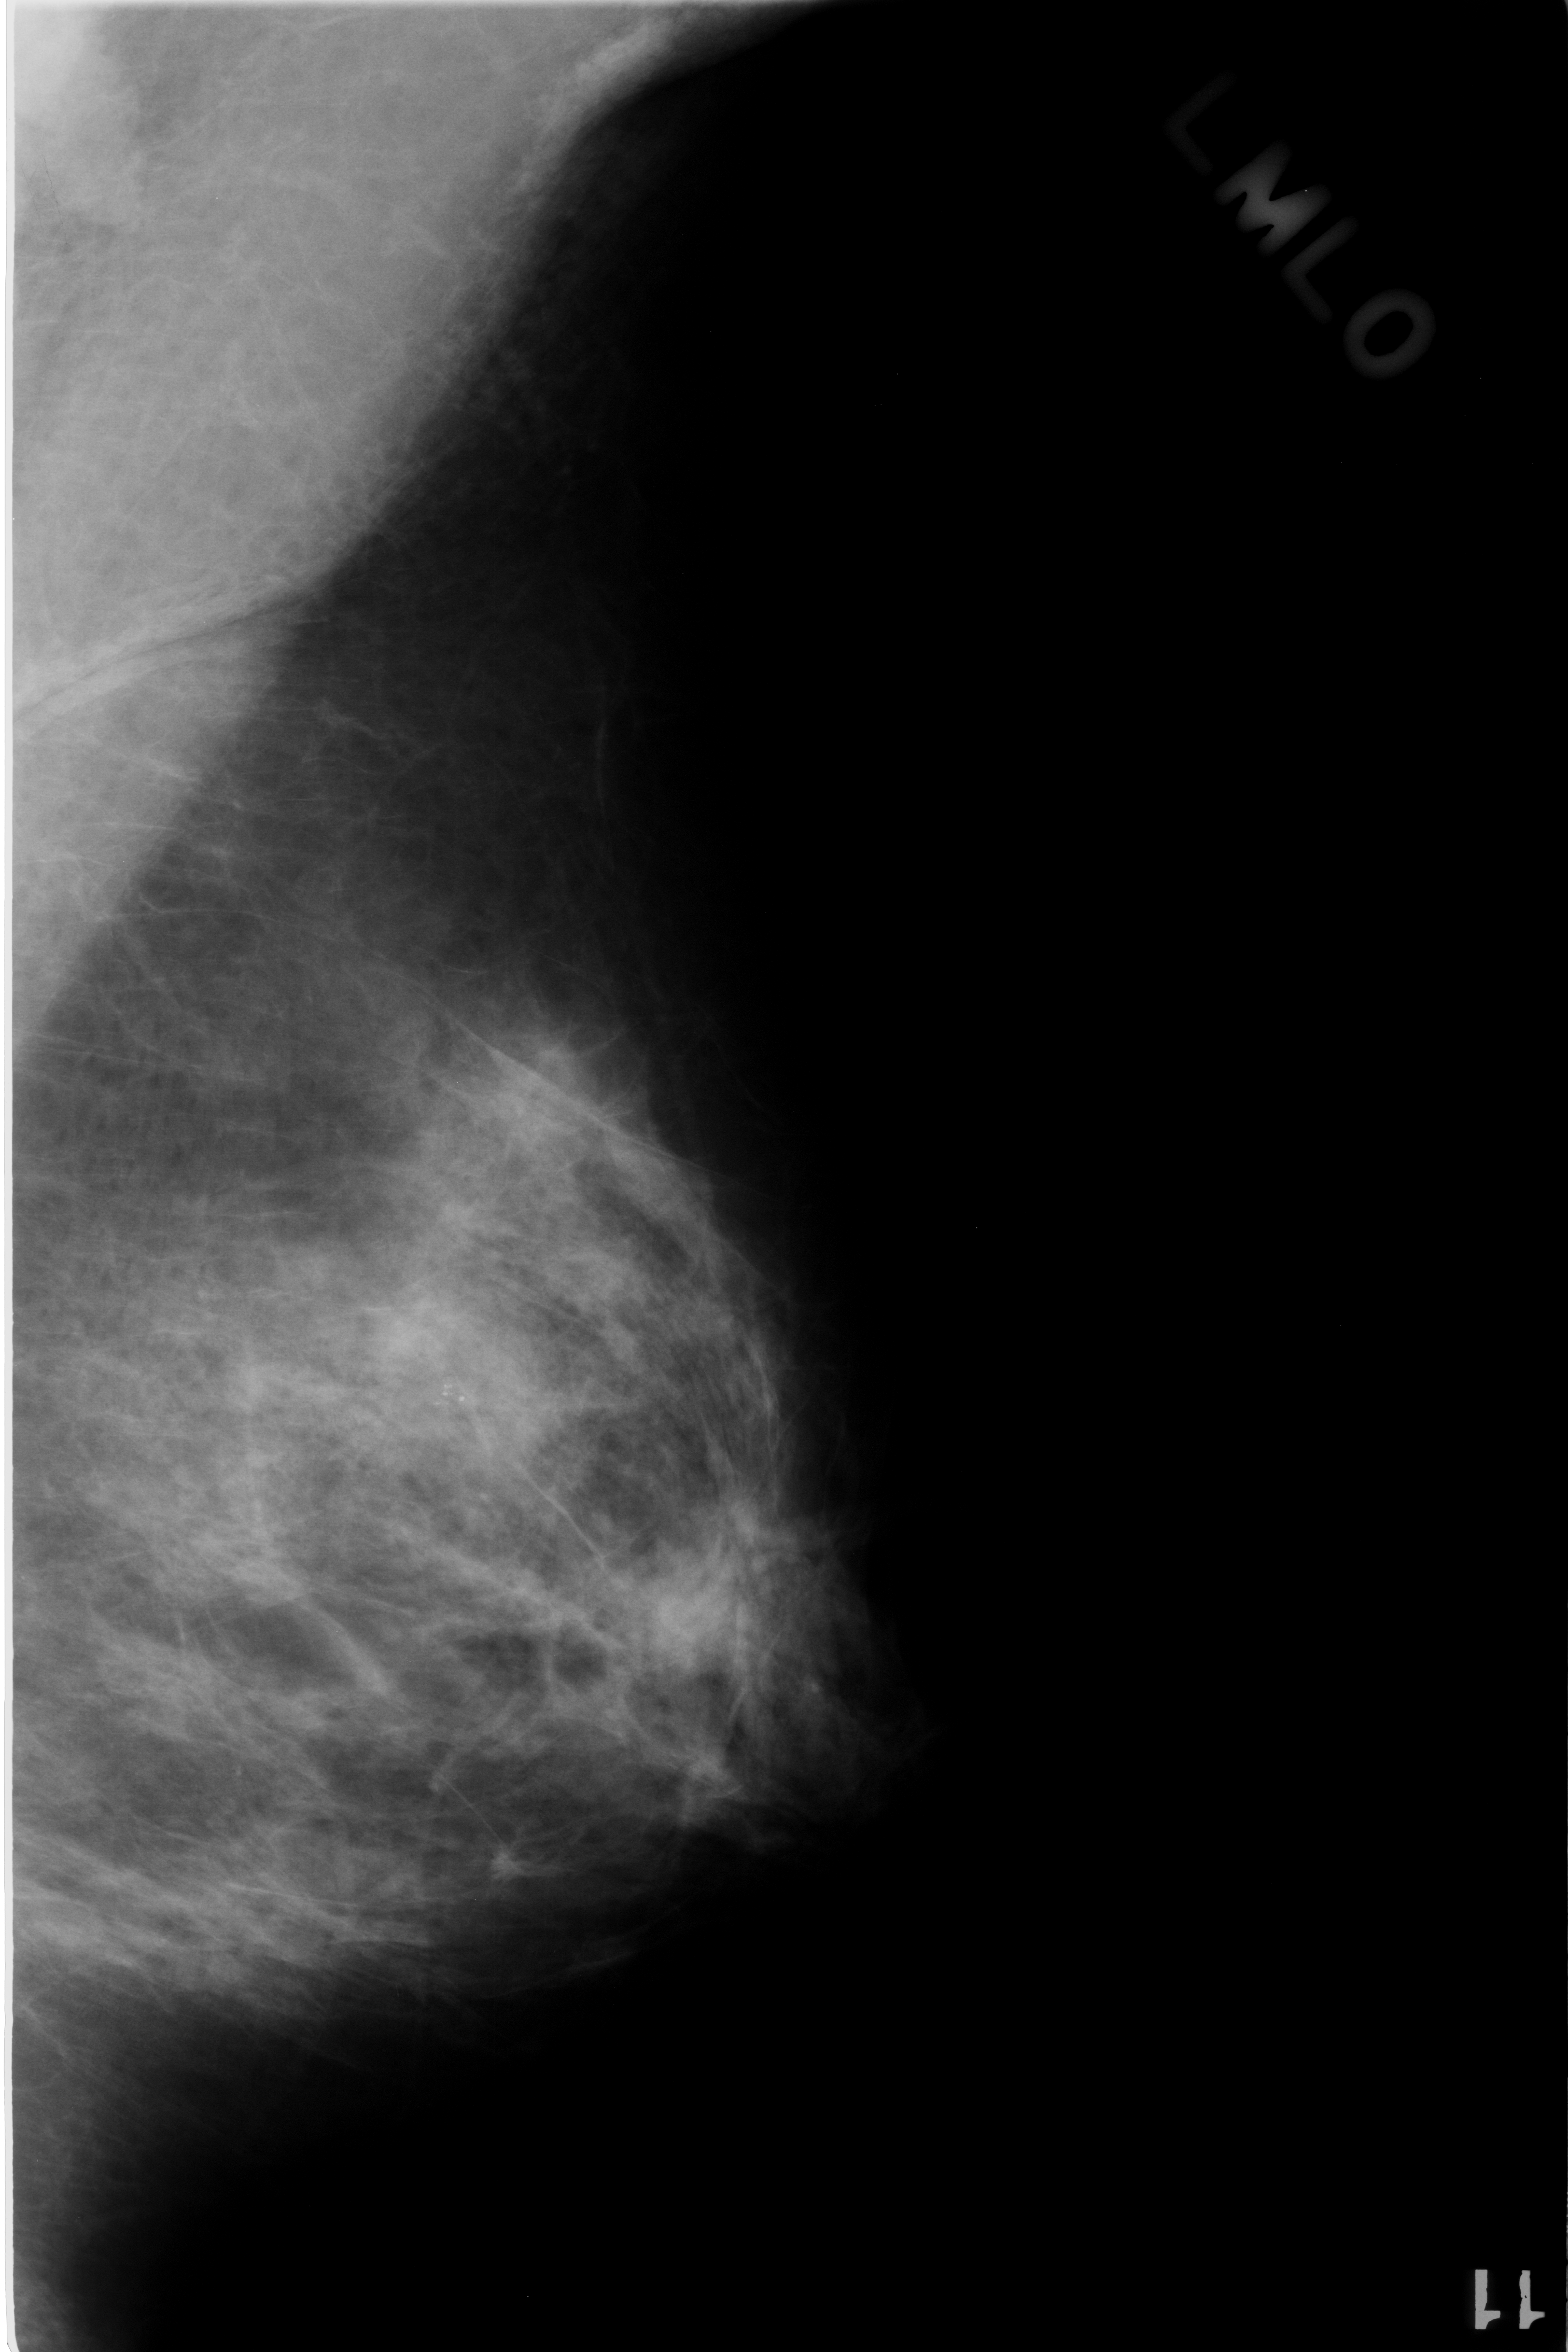
Digitized screen-film mammogram; left breast; mediolateral oblique (MLO) view.
Calcifications, morphology punctate, distribution clustered; BI-RADS assessment category 3; pathology (as recorded): benign.